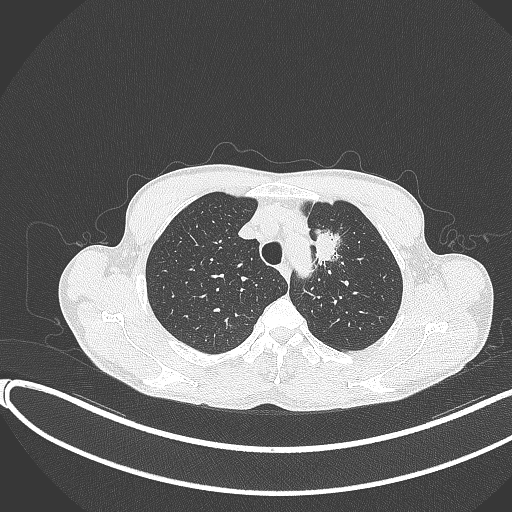
Chest CT, one axial slice; position 309 of 374 along the scan axis; reconstruction kernel B70f; 120 kVp; lung window (W 1500 / L -600 HU); 1 mm slice thickness; 512 × 512 image matrix, field of view 400 × 400 mm. Male patient, age 58 years. From the clinical record (not read from this slice): clinical TNM (as recorded): T1c N1 M0.
Outlined on this slice (rectangle marked by the reading radiologist):
- lung tumour (recorded histology: adenocarcinoma): bounding box [x1, y1, x2, y2] px = [306, 226, 345, 271]